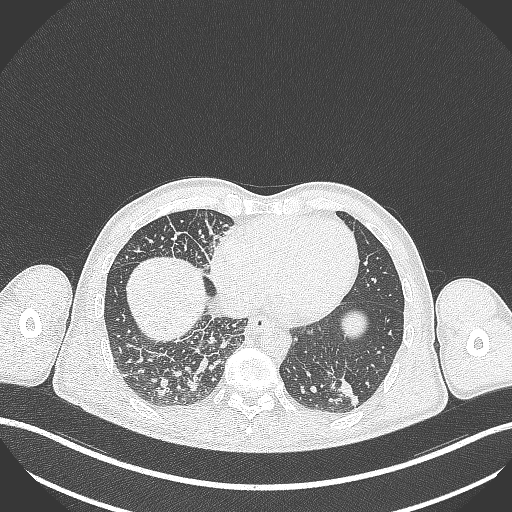
Chest CT, one axial slice; position 88 of 348 along the scan axis; reconstruction kernel B70f; 120 kVp; lung window (W 1500 / L -600 HU); 1 mm slice thickness; 512 × 512 image matrix. Male patient, age 49 years. Case-level facts recorded for this patient, not image findings: clinical TNM (as recorded): T2b N1 M0.
Outlined on this slice (bounding box drawn by a radiologist):
- lung tumour (recorded histology: adenocarcinoma): bounding box <335,376,362,407> (left, top, right, bottom; pixels)